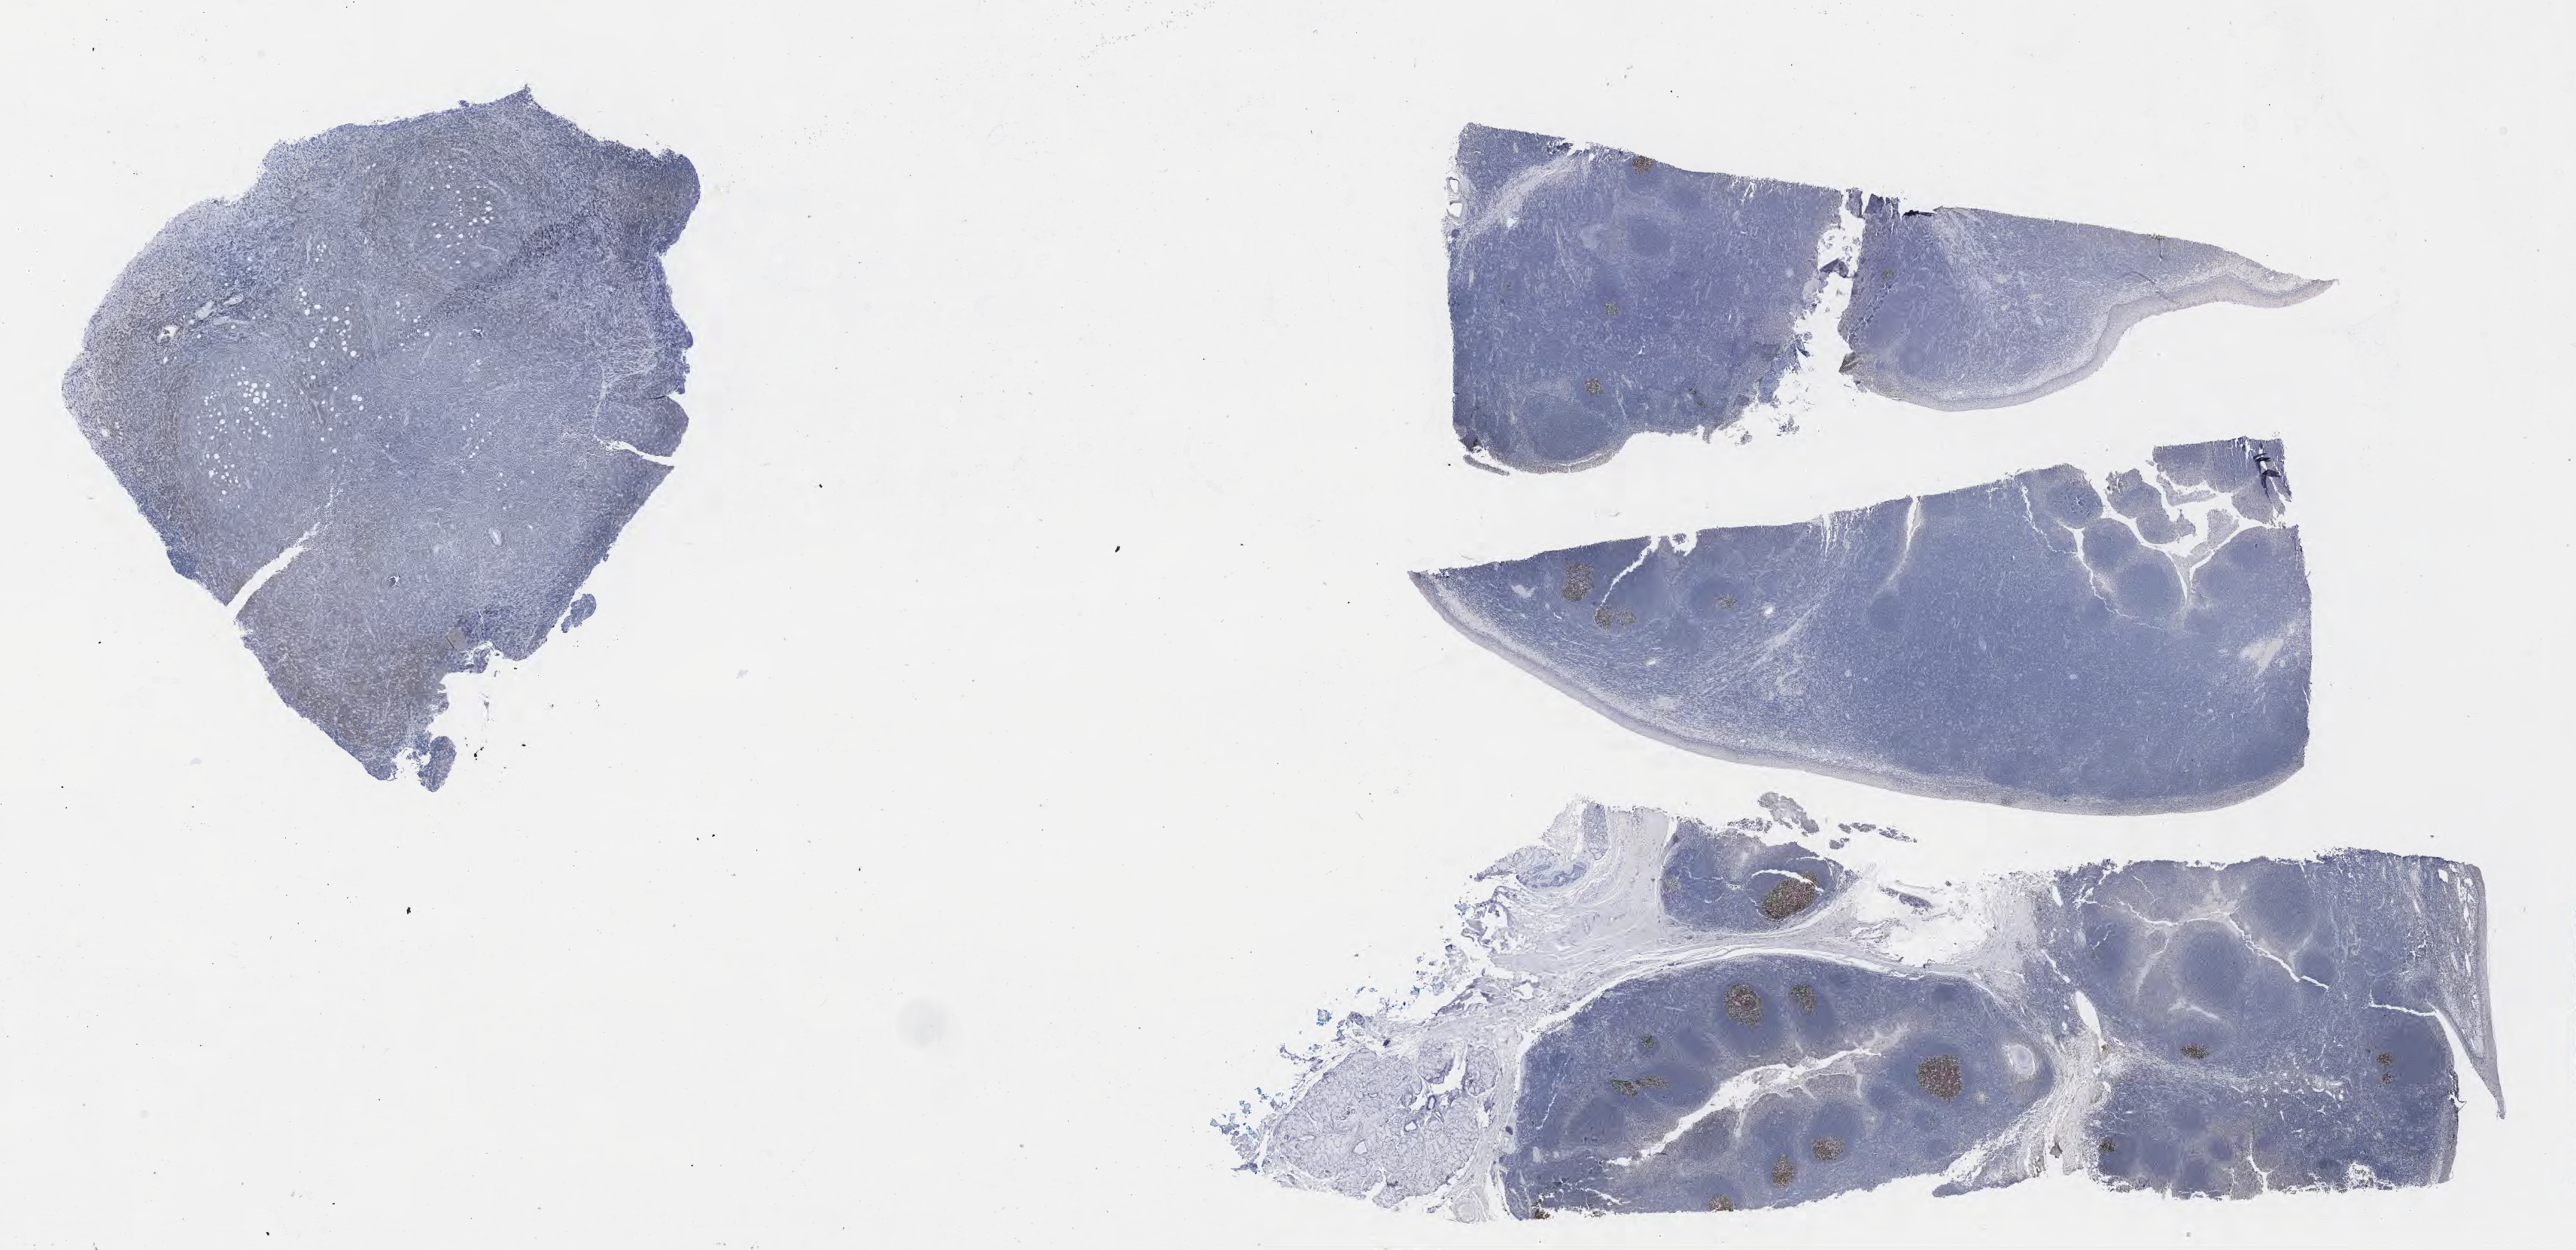
IHC for BCL6, whole-slide image, whole scanned area (about 27.7 x 13.4 mm) shown as a low-resolution overview; specimen: tumor tissue; anatomic site: retroperitoneum. Male, age 7 years at initial diagnosis.
Diagnosis: Diffuse large B-cell lymphoma, NOS.